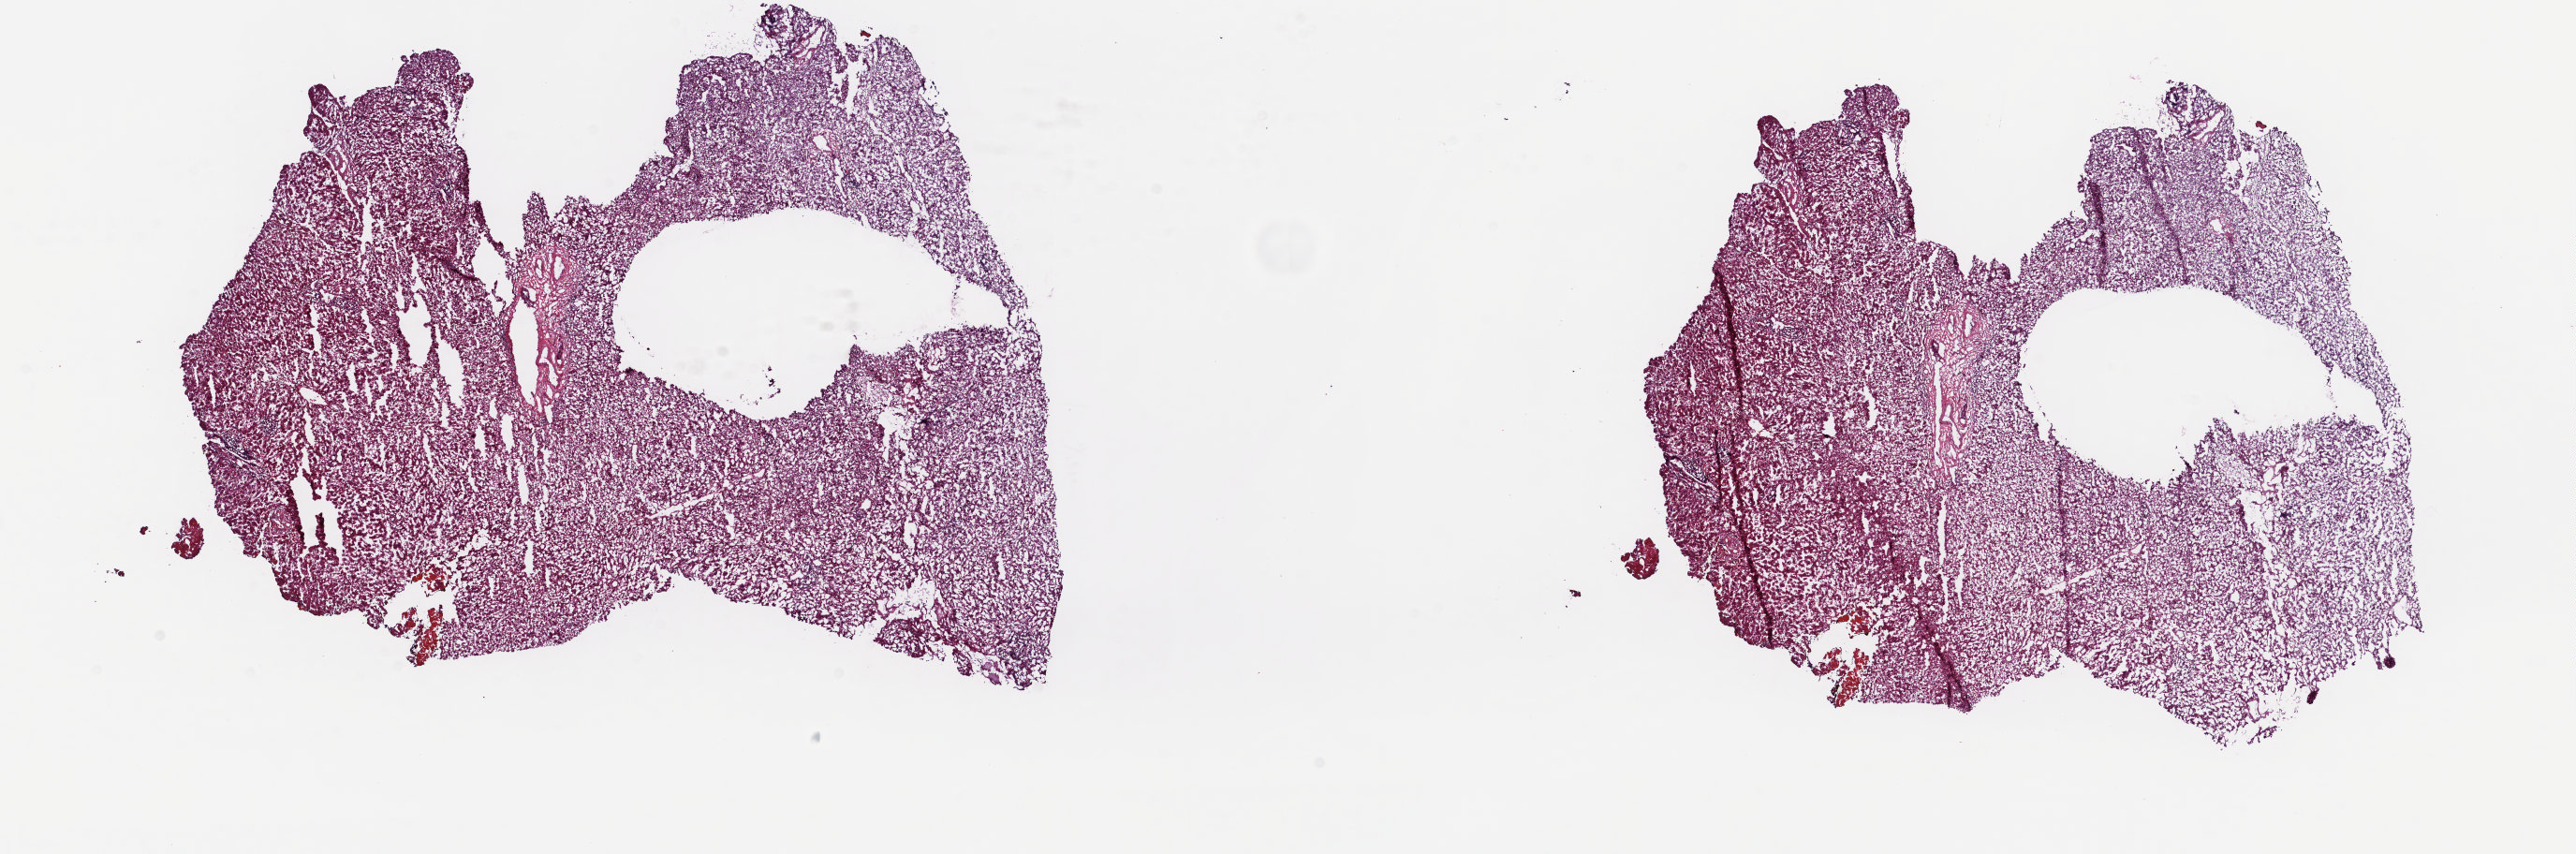
Hematoxylin and eosin (H&E) stained whole-slide image, low-resolution overview of the scanned area, about 21.8 x 7.2 mm (acquisition: 20x scan). Frozen section from the top of the tissue portion. Solid tissue normal (non-tumour tissue) sample from the liver. Patient: female, age at initial diagnosis 57 years. Pathologist review of this section (percent, as recorded): tumour cells 0%, tumour nuclei 0%, normal cells 100%, stromal cells 0%, necrosis 0%. Inflammatory infiltration, as recorded: lymphocyte infiltration 0%, monocyte infiltration 0%, neutrophil infiltration 0%.
This section: solid tissue normal sample (biorepository sample class). Patient diagnosis: Hepatocellular carcinoma, NOS.